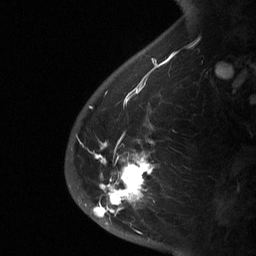
Breast MRI (dynamic contrast-enhanced), one sagittal slice. Dynamic contrast-enhanced study with each time point stored as its own series, time point 2 of 3 at this slice position (early post-contrast, ordered by acquisition time). 1.5 T. TE 4.8 ms, TR 27 ms. 2 mm slice thickness. 256 × 256 image matrix, field of view 180 × 180 mm. Patient: female, 56 years. From the clinical record (not read from this slice): setting: breast cancer imaged before/during neoadjuvant chemotherapy; receptor status: HER2-positive.
Annotated regions visible in this slice (semi-automatic segmentation, software-assisted and operator-edited):
- analysis volume of interest (the breast-tissue region the enhancement analysis was run in; not a lesion): box from (x=65, y=137) to (x=182, y=229) px
- tumour enhancement mask (voxels above the 90 % enhancement threshold inside the analysis volume of interest): (x=93, y=141)–(x=154, y=217)